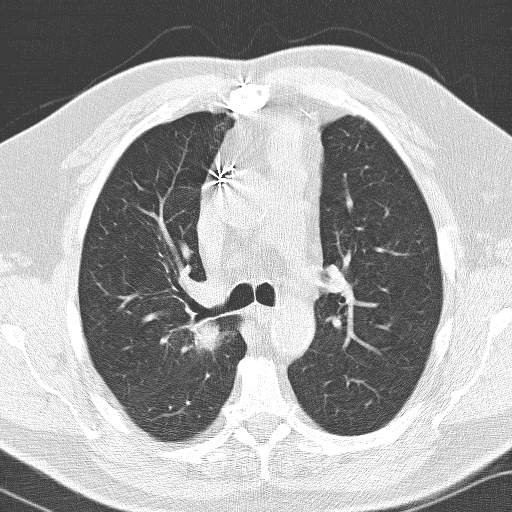
Chest CT (low-dose screening protocol), one axial image. Baseline annual screen. Lung window (W 1500 / L -600 HU). 3.2 mm slice thickness. Lung (sharp) reconstruction kernel (D). Slice 42 of 141 in the series. 512 × 512 image matrix, field of view 326 × 326 mm. Male participant, aged 66 years at enrolment. Former smoker at enrolment.
Expert-annotated lung lesion, box from (x=145, y=291) to (x=232, y=389) px. The exam's reader record, not a measurement of the box and not confirmed to be the same lesion: non-calcified nodule or mass ≥4 mm, right upper lobe, 36 × 30 mm, spiculated (stellate) margins, soft tissue attenuation. Official screen result: positive, change unspecified: nodule(s) >= 4 mm or enlarging nodule(s), mass(es), or other non-specific abnormalities suspicious for lung cancer. Lung cancer was diagnosed 103 days after this screen: adenocarcinoma, NOS, right upper lobe, poorly differentiated (G3), stage IIB (AJCC 6th edition), 33 mm at pathology.